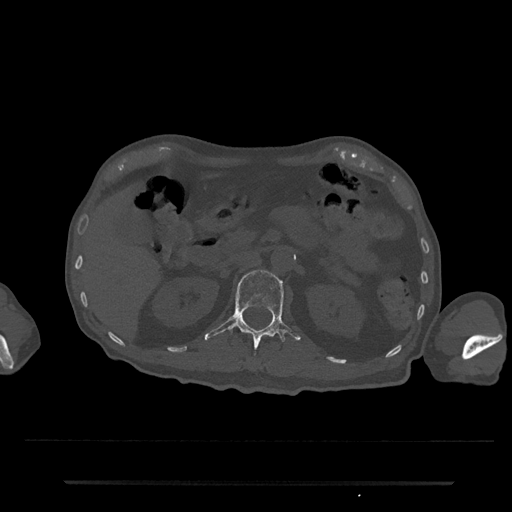
CT including the spine, one axial slice; slice 131 of 797 in the series (ordered by position); reconstruction kernel Br40s/3; 120 kVp; bone window (W 1800 / L 400 HU); 0.5 mm slice thickness; 512 × 512 image matrix. Patient: male, 74 years. Case-level facts recorded for this patient, not image findings: primary cancer: prostate.
Structures marked on this image (semi-automatically segmented with operator editing):
- L1 vertebra: bounding box [x1, y1, x2, y2] px = [204, 270, 301, 348]